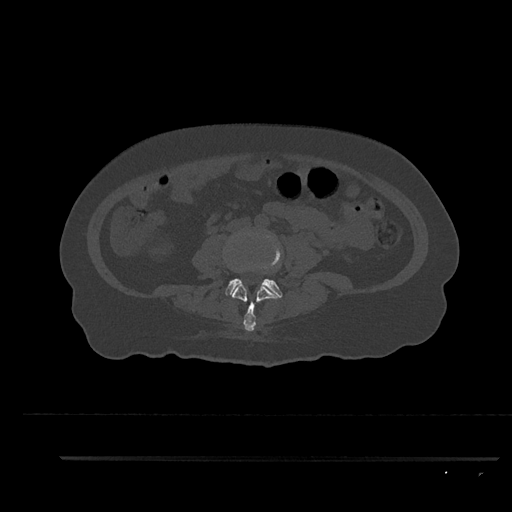
CT including the spine, one axial slice. Slice 52 of 797 in the series (ordered by position). Bone window (W 1800 / L 400 HU). 0.5 mm slice thickness. 512 × 512 image matrix, field of view 408 × 408 mm. Patient: female, 44 years. From the clinical record (not read from this slice): primary cancer: renal; vertebrae with lytic lesions (as recorded): L1.
Structures marked on this image (semi-automatic segmentation, software-assisted and operator-edited):
- L3 vertebra: bounding box <232,284,282,331> (left, top, right, bottom; pixels)
- L4 vertebra: <225,235,282,297>